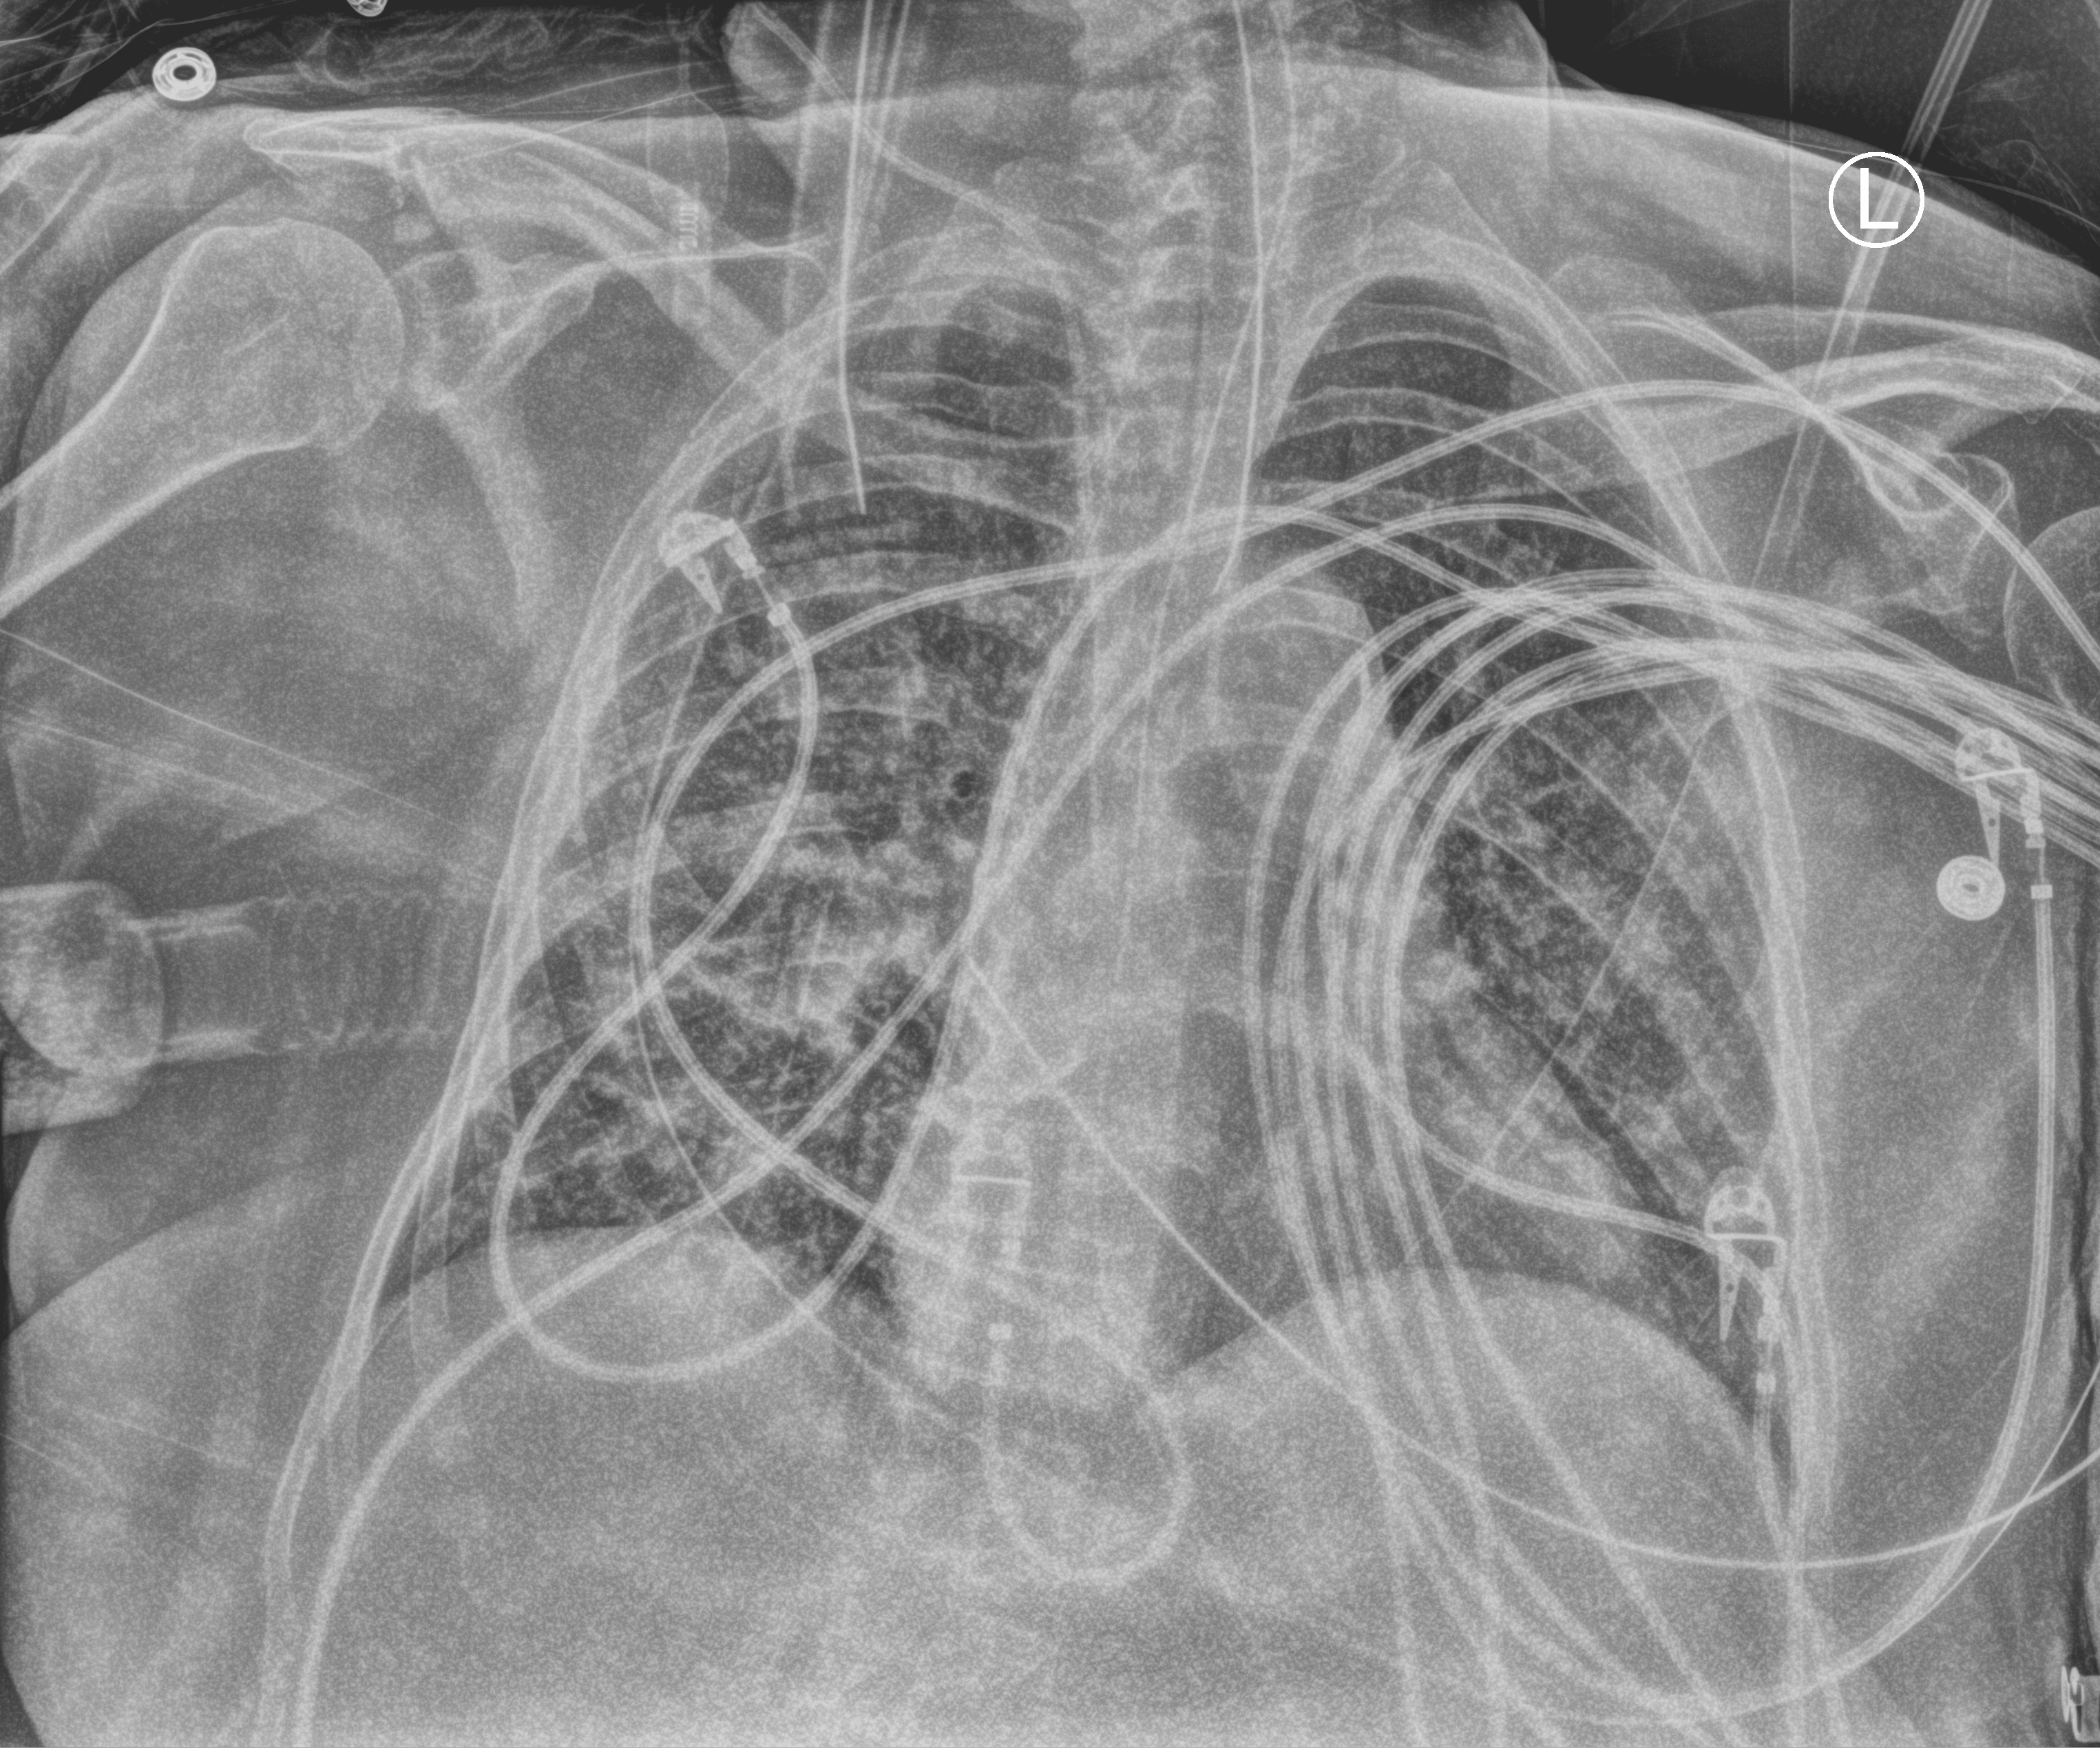
Portable chest radiograph, anteroposterior (AP) projection. Female patient hospitalised with COVID-19, age 75–90 years.
From the hospital-stay record, not from the radiograph (when in the stay this image was taken is not recorded): length of hospital stay: 31 days.